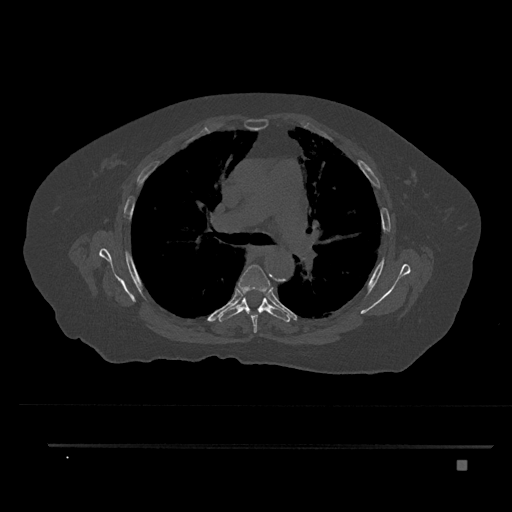
CT including the spine, one axial slice. Position 546 of 797 along the scan axis. 120 kVp. Bone window (W 1800 / L 400 HU). 0.5 mm slice thickness. 512 × 512 image matrix, field of view 437 × 437 mm. Patient: female, 76 years. From the clinical record (not read from this slice): primary cancer: lung.
Structures marked on this image (semi-automatically segmented with operator editing):
- T5 vertebra: box from (x=238, y=265) to (x=271, y=333) px
- T6 vertebra: (x=219, y=290)–(x=290, y=322)